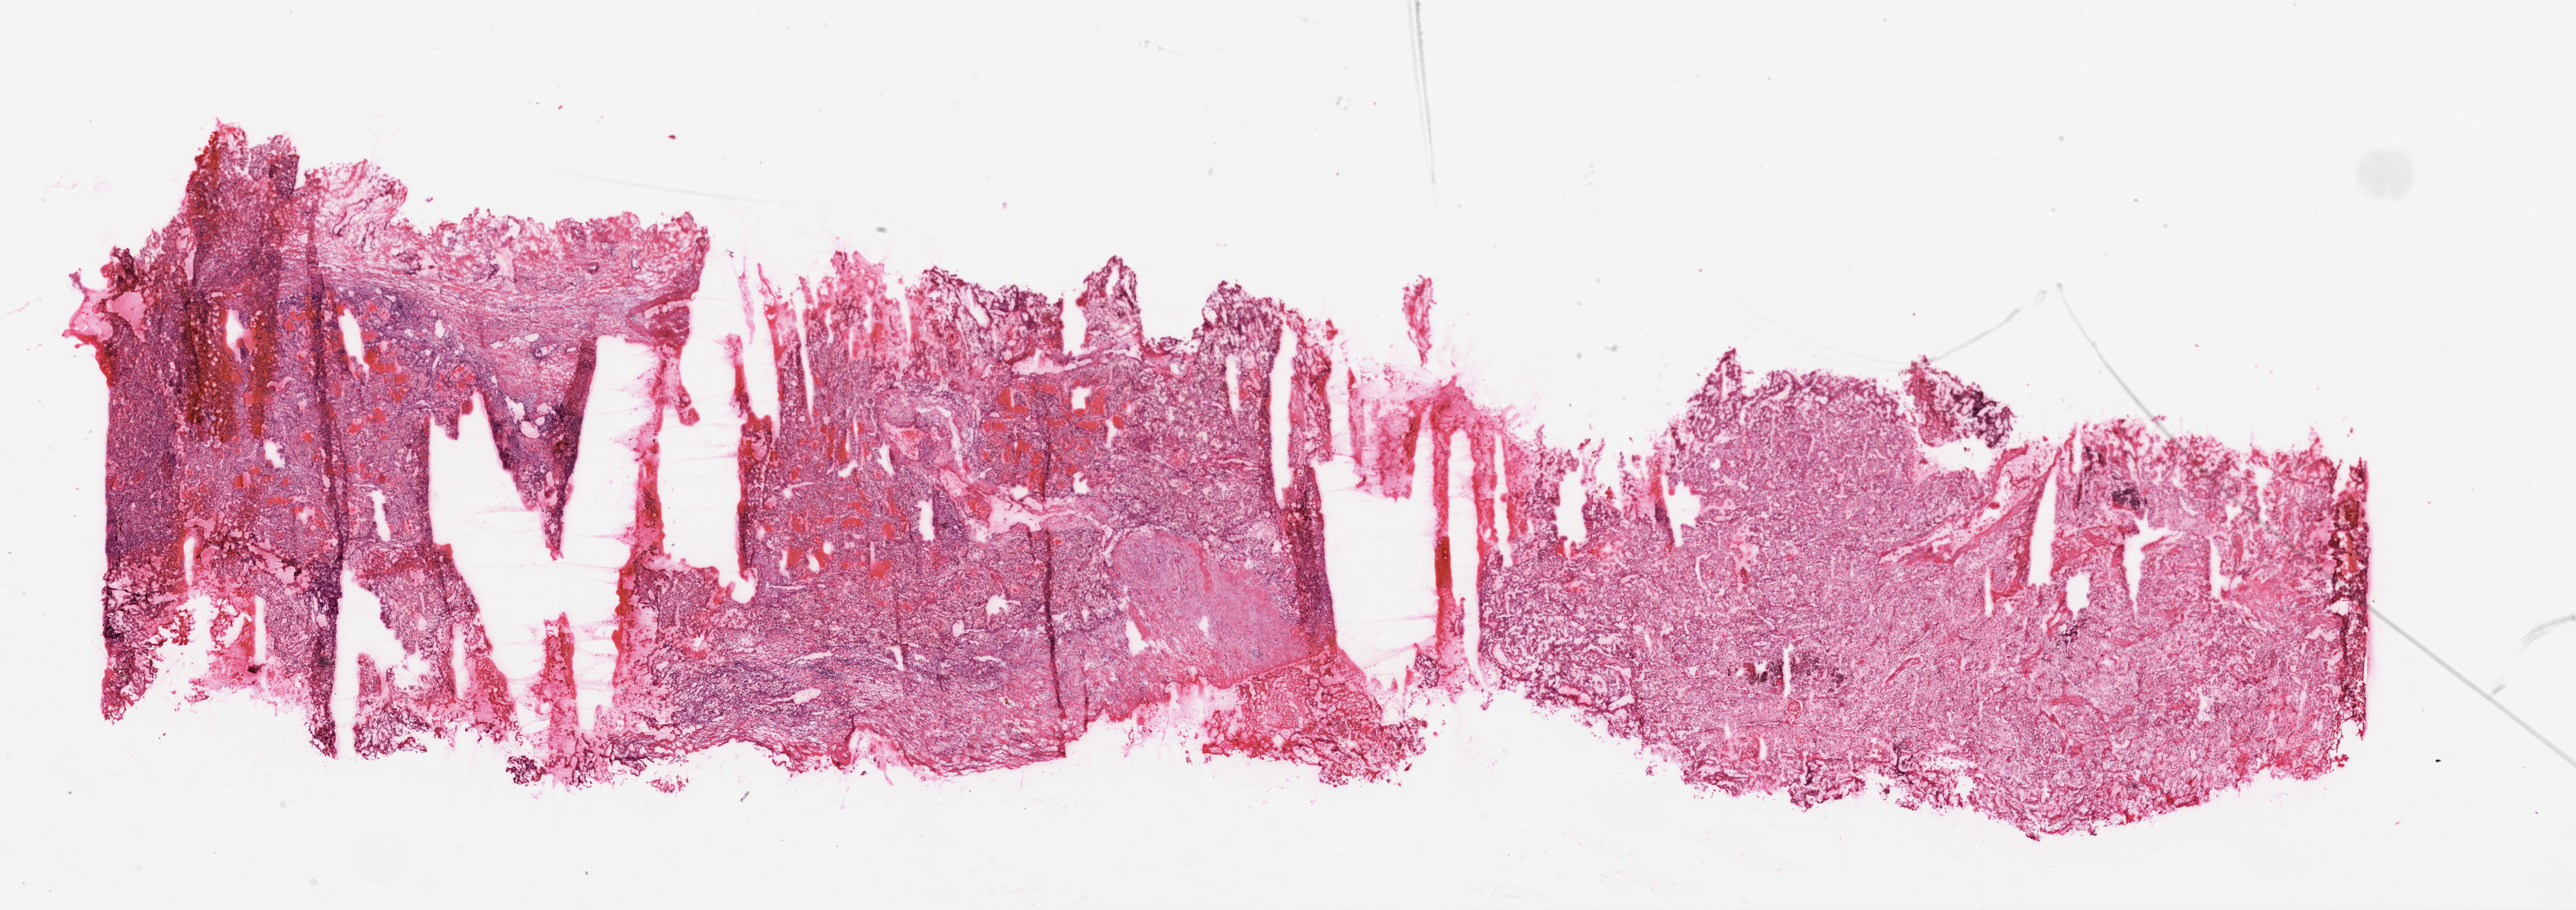
Whole-slide histology image, H&E-stained, shown as a low-resolution overview of the whole scanned area (about 27.1 x 9.6 mm, acquisition: 20x scan); frozen section from the top of the tissue portion; primary tumour sample from the kidney. Male, age 61 years at initial diagnosis. Histologic grade: G3 (poorly differentiated). Pathologist review of this section (percent, as recorded): tumour cells 80%, tumour nuclei 75%, normal cells 0%, stromal cells 20%, necrosis 0%.
Laterality: right. Diagnosis: Clear cell adenocarcinoma, NOS. TNM: T3a NX M0. AJCC pathologic stage: III.